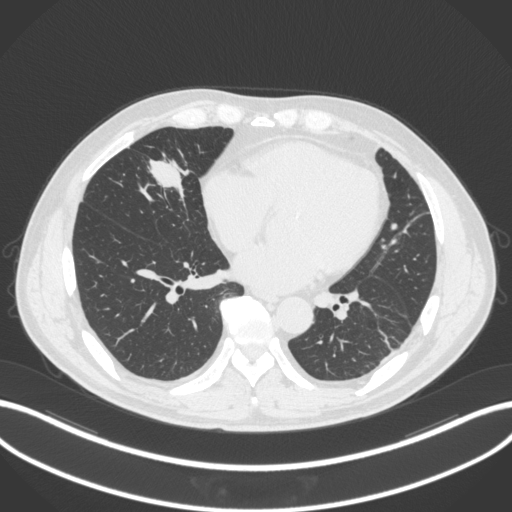
Chest CT, one axial slice. Slice 107 of 399 in the series (ordered by position). 120 kVp. Lung window (W 1500 / L -600 HU). 1 mm slice thickness. 512 × 512 image matrix. Patient: male, 59 years. From the clinical record (not read from this slice): clinical TNM (as recorded): T2a N1 M0.
Annotated regions visible in this slice (bounding box drawn by a radiologist):
- lung tumour (recorded histology: adenocarcinoma): bounding box <144,155,190,200> (left, top, right, bottom; pixels)